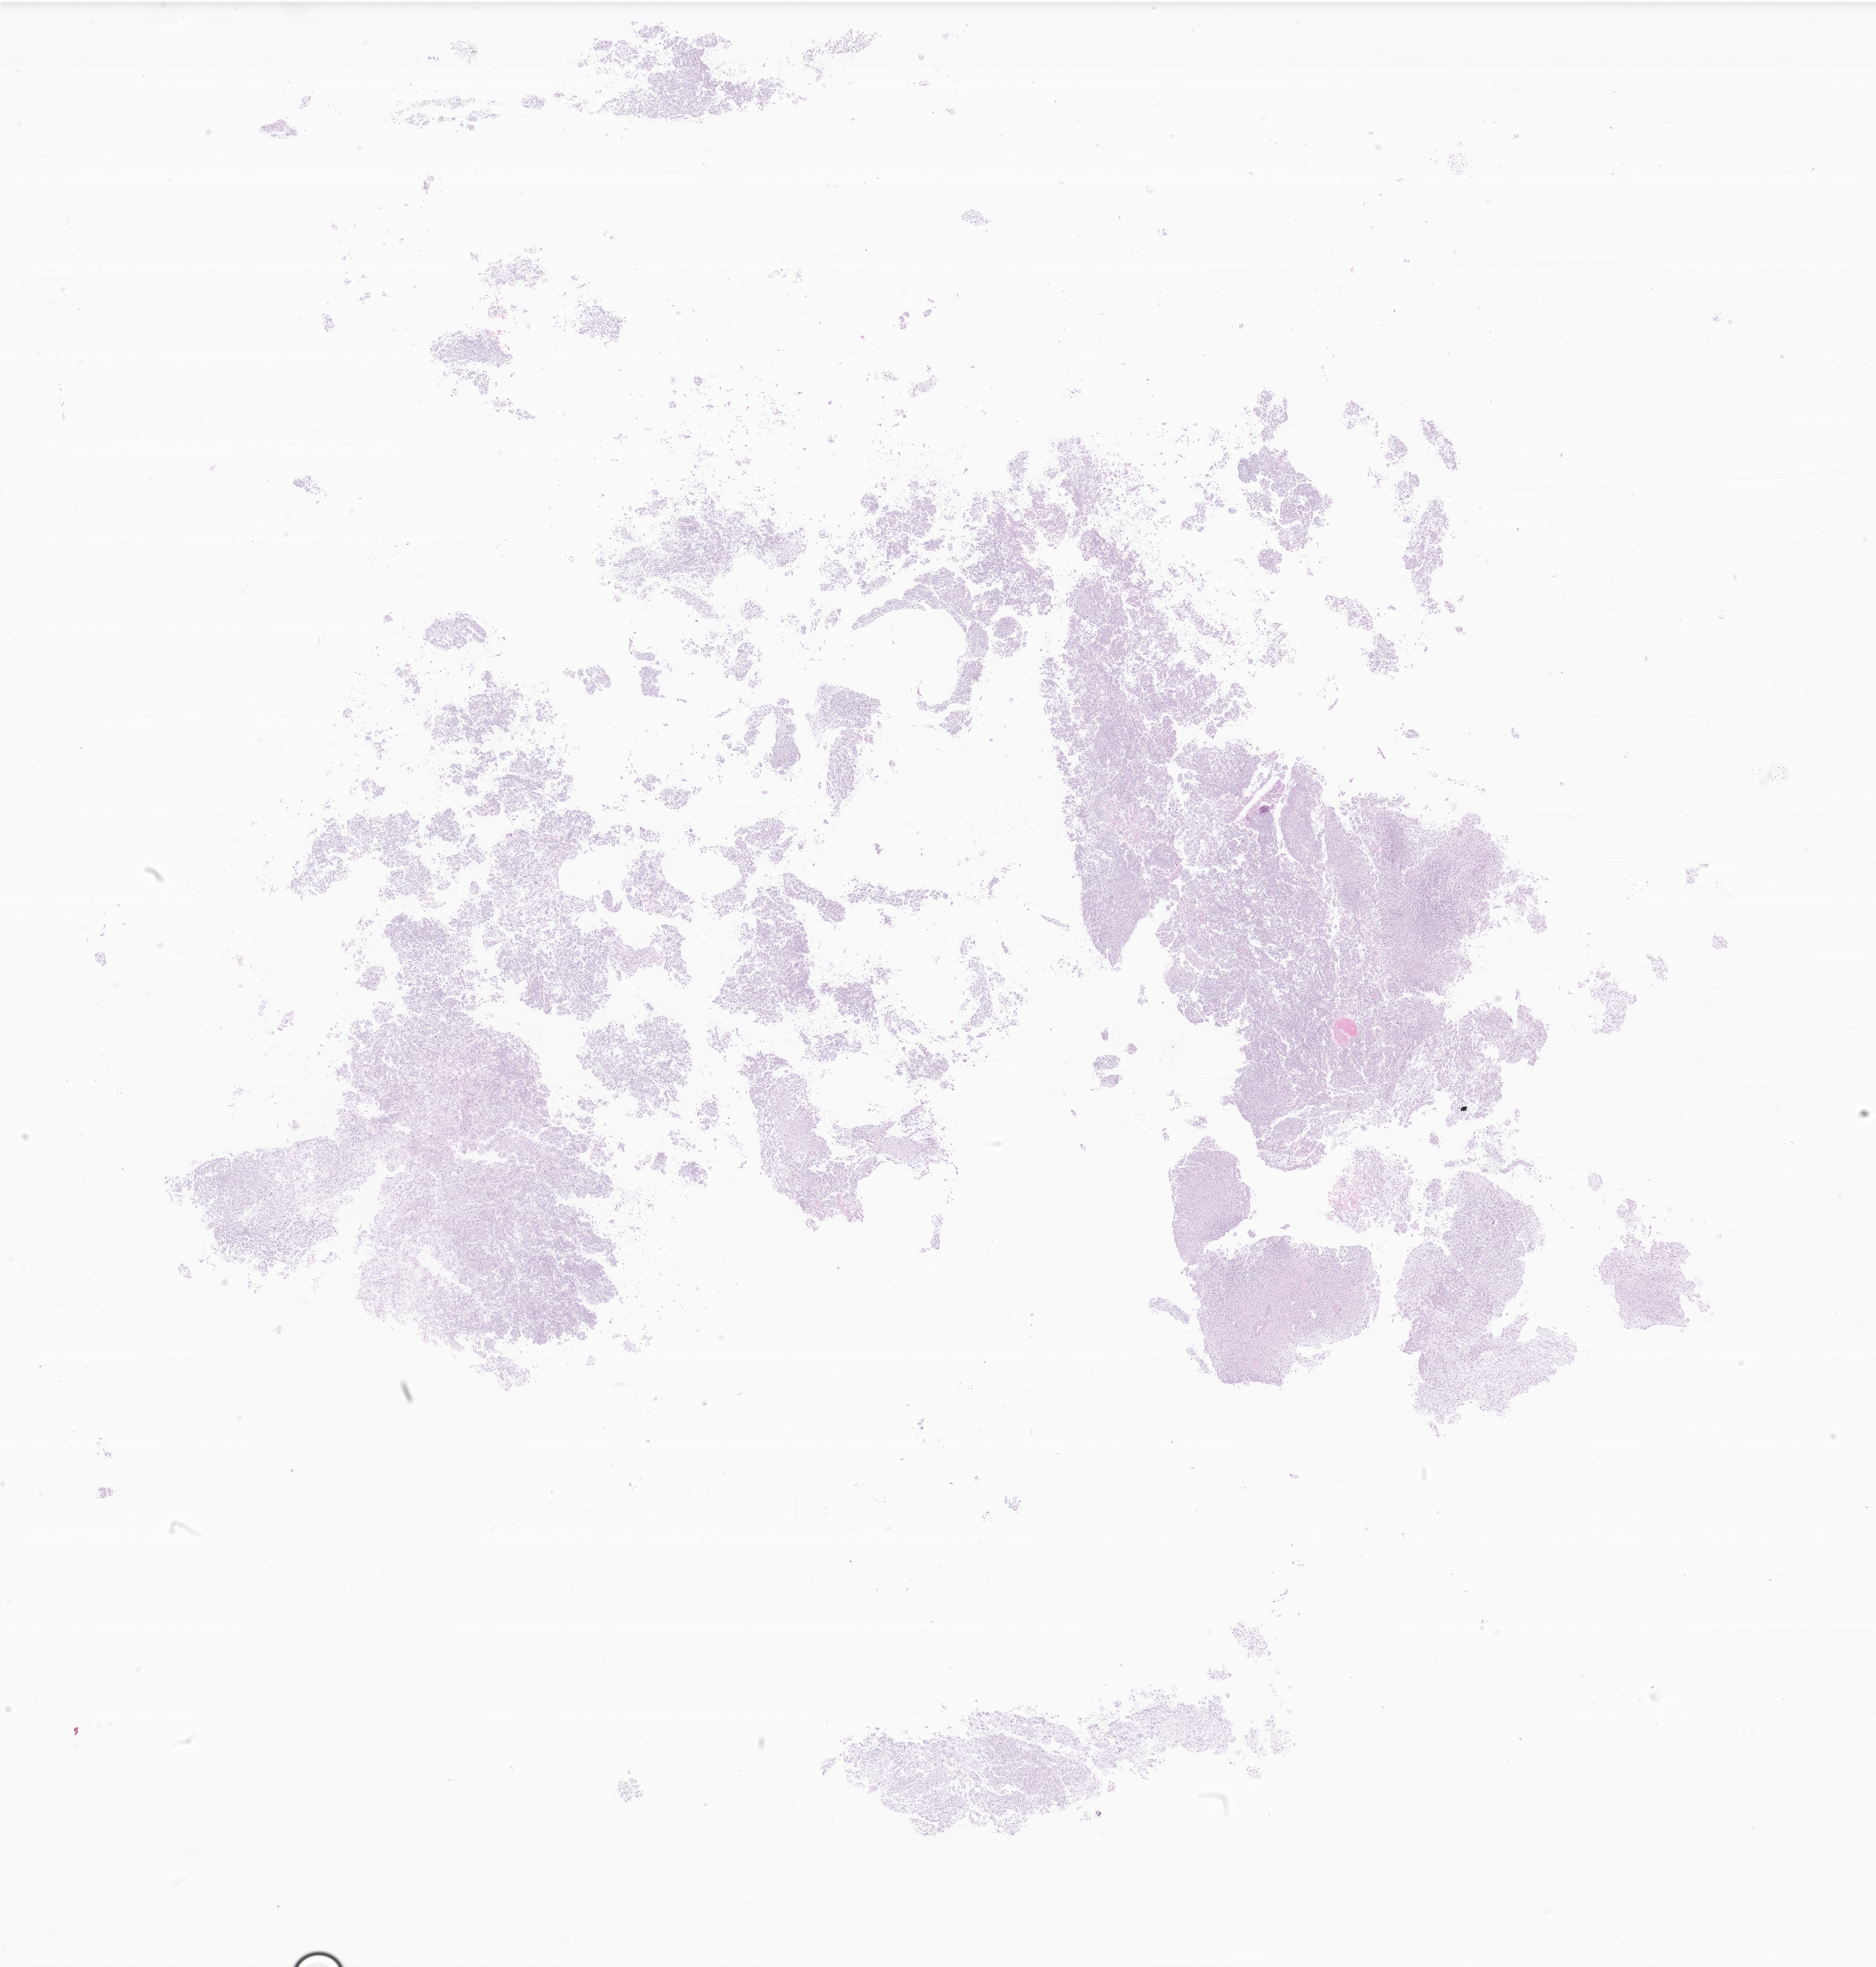
Digitized hematoxylin and eosin (H&E)-stained section of tumor tissue from the brain, a low-resolution overview of the entire scanned area, about 22.1 x 23.2 mm; formalin-fixed paraffin-embedded section. Patient: female, age 63 days.
- diagnosis: Pilocytic astrocytoma